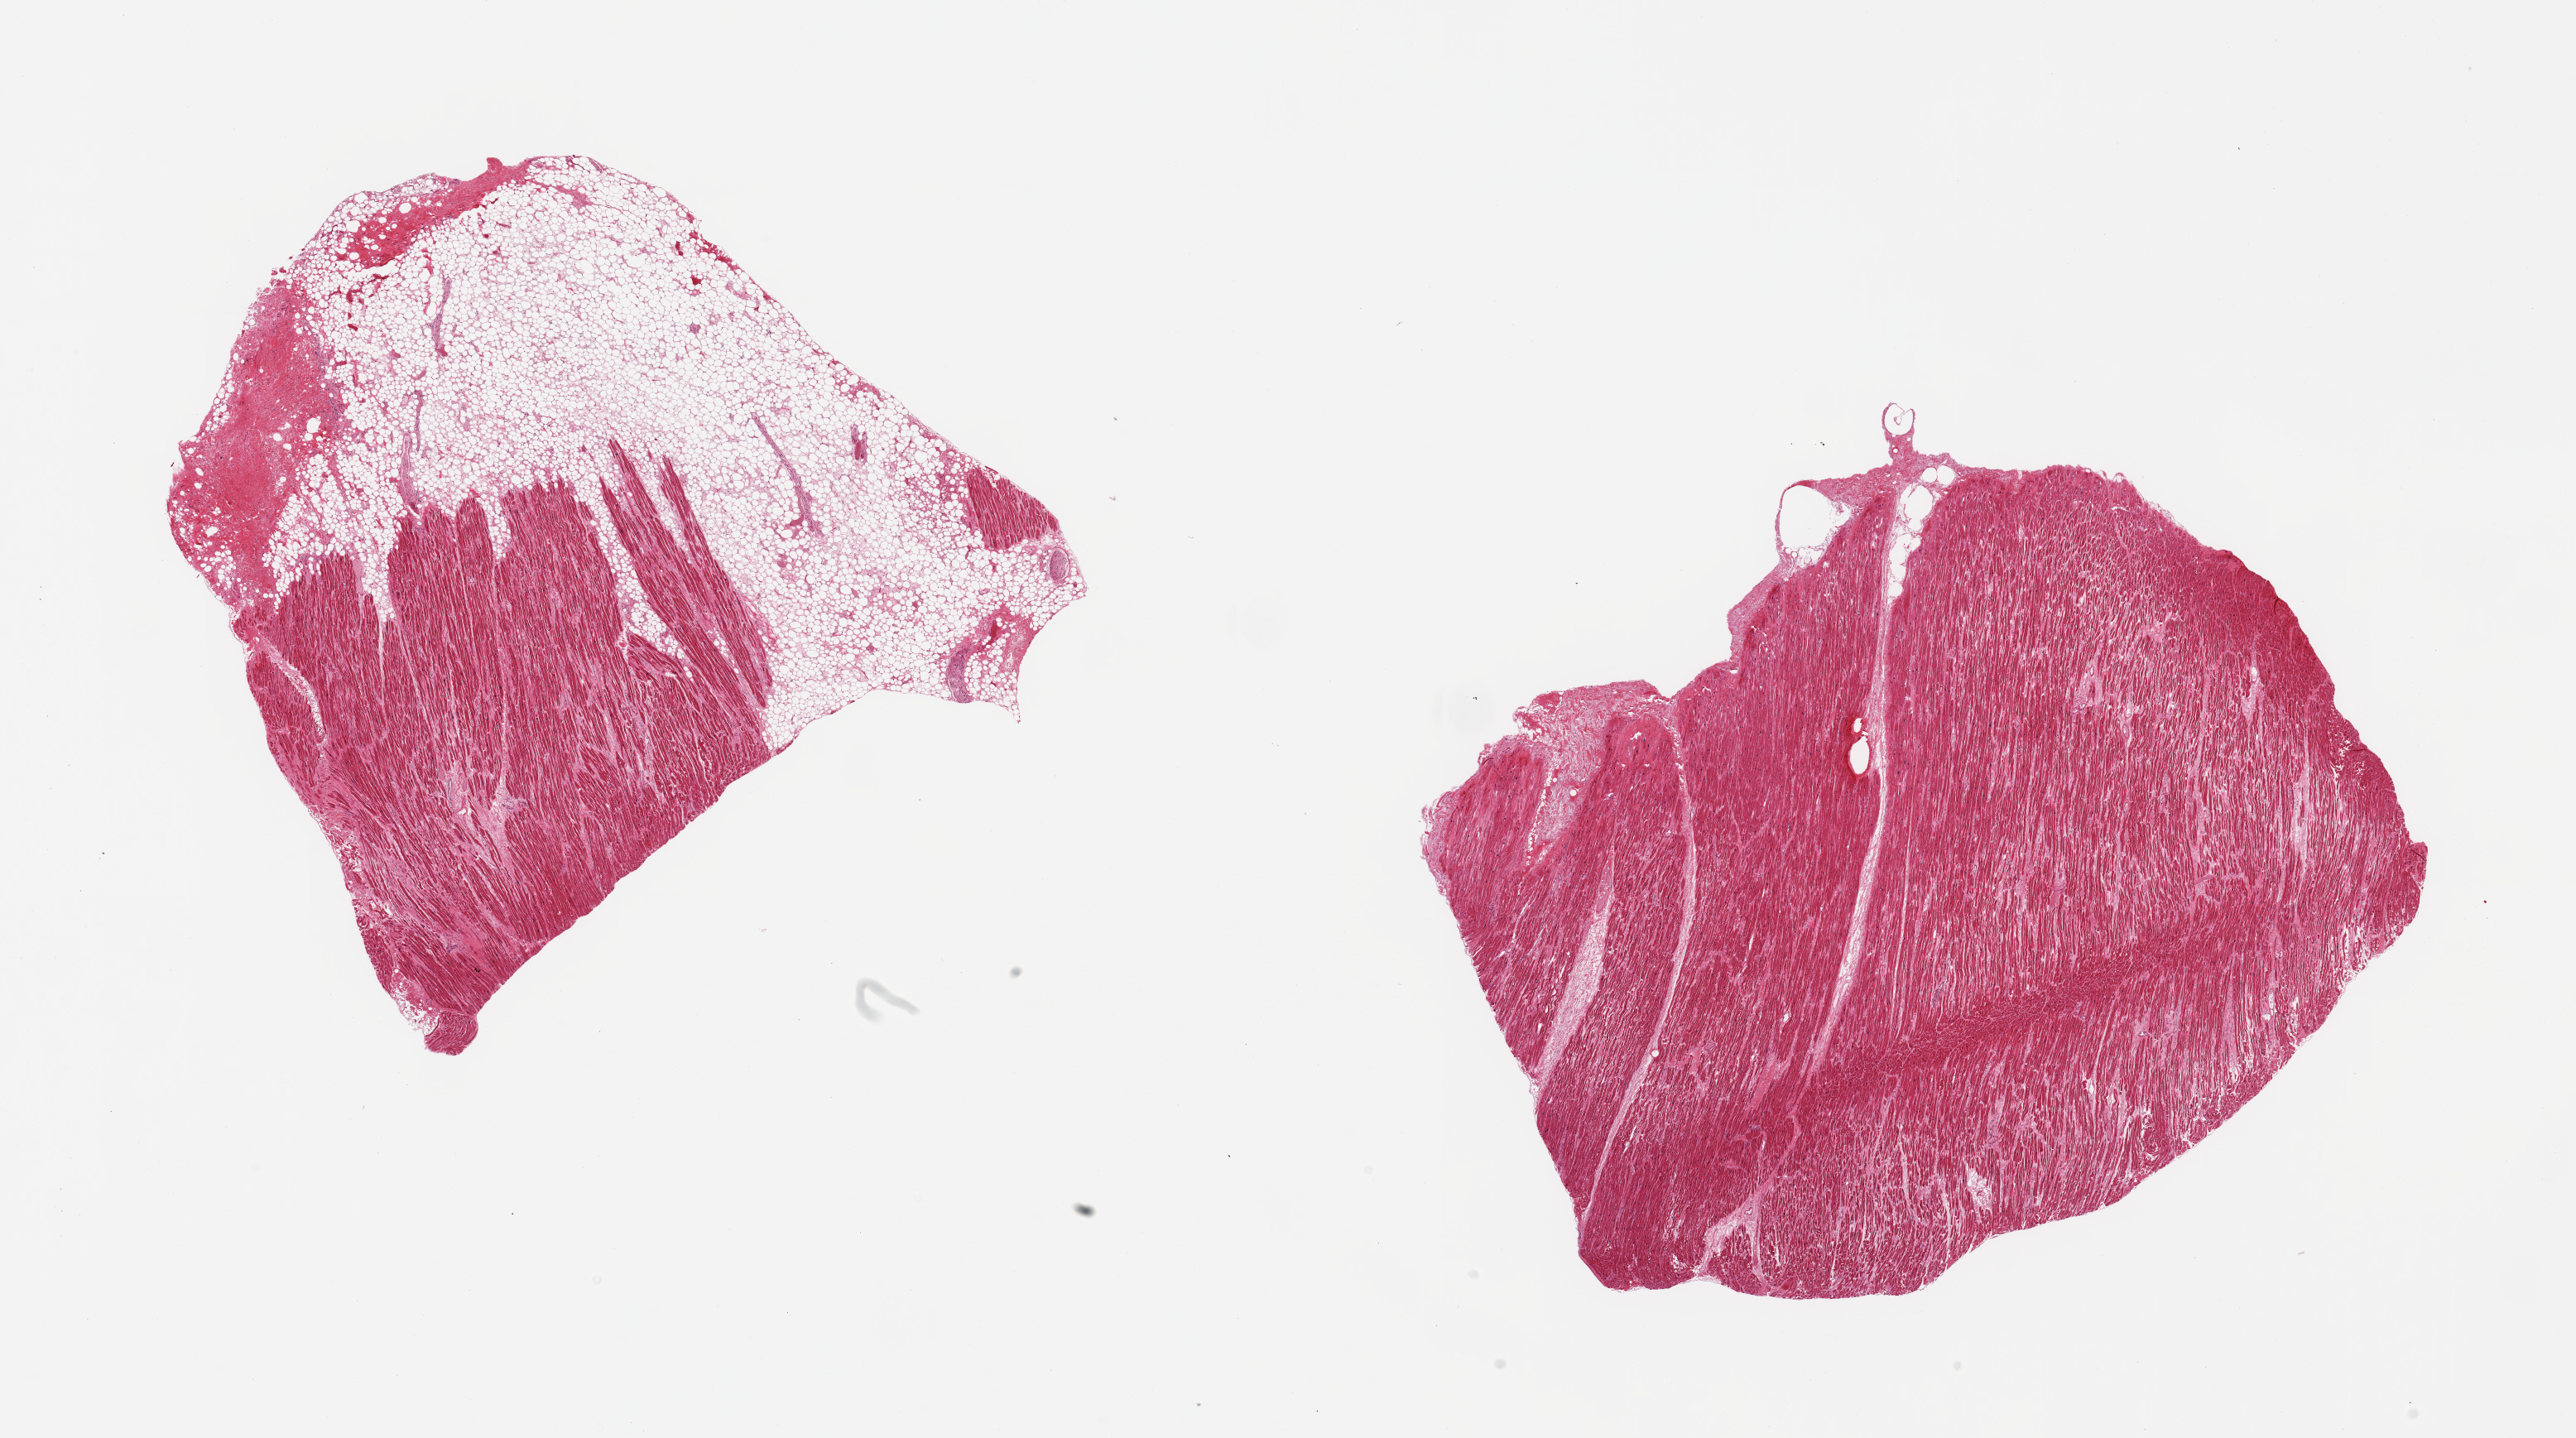
Digitized hematoxylin and eosin (H&E)-stained section, low-resolution overview of the scanned area, about 24.6 x 13.7 mm (slide scanned at 20x), PAXgene-fixed paraffin-embedded (PFPE) section, target tissue: auricular appendage, donor tissue sample. Male donor.
* review note (as recorded): 2 pieces; 1 piece has large fibrofatty layer occupying 50%